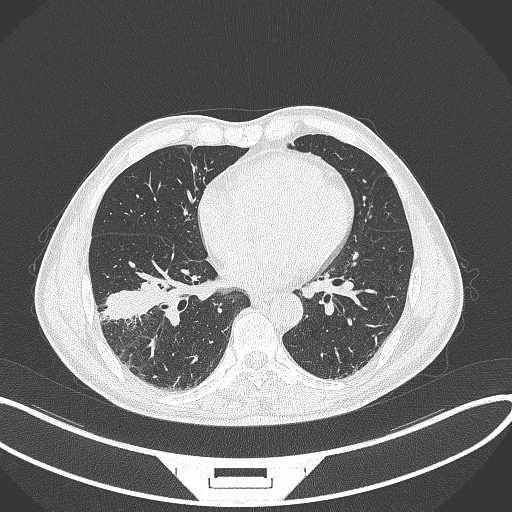
Chest CT, one axial slice; position 145 of 364 along the scan axis; reconstruction kernel B70f; 120 kVp; lung window (W 1500 / L -600 HU); 1 mm slice thickness; 512 × 512 image matrix, field of view 400 × 400 mm. Patient: male, 58 years. From the clinical record (not read from this slice): clinical TNM (as recorded): T3 N0 M0; histopathological grade: G2.
Annotated regions visible in this slice (rectangle marked by the reading radiologist):
- lung tumour (recorded histology: squamous cell carcinoma): bounding box <96,273,171,322> (left, top, right, bottom; pixels)